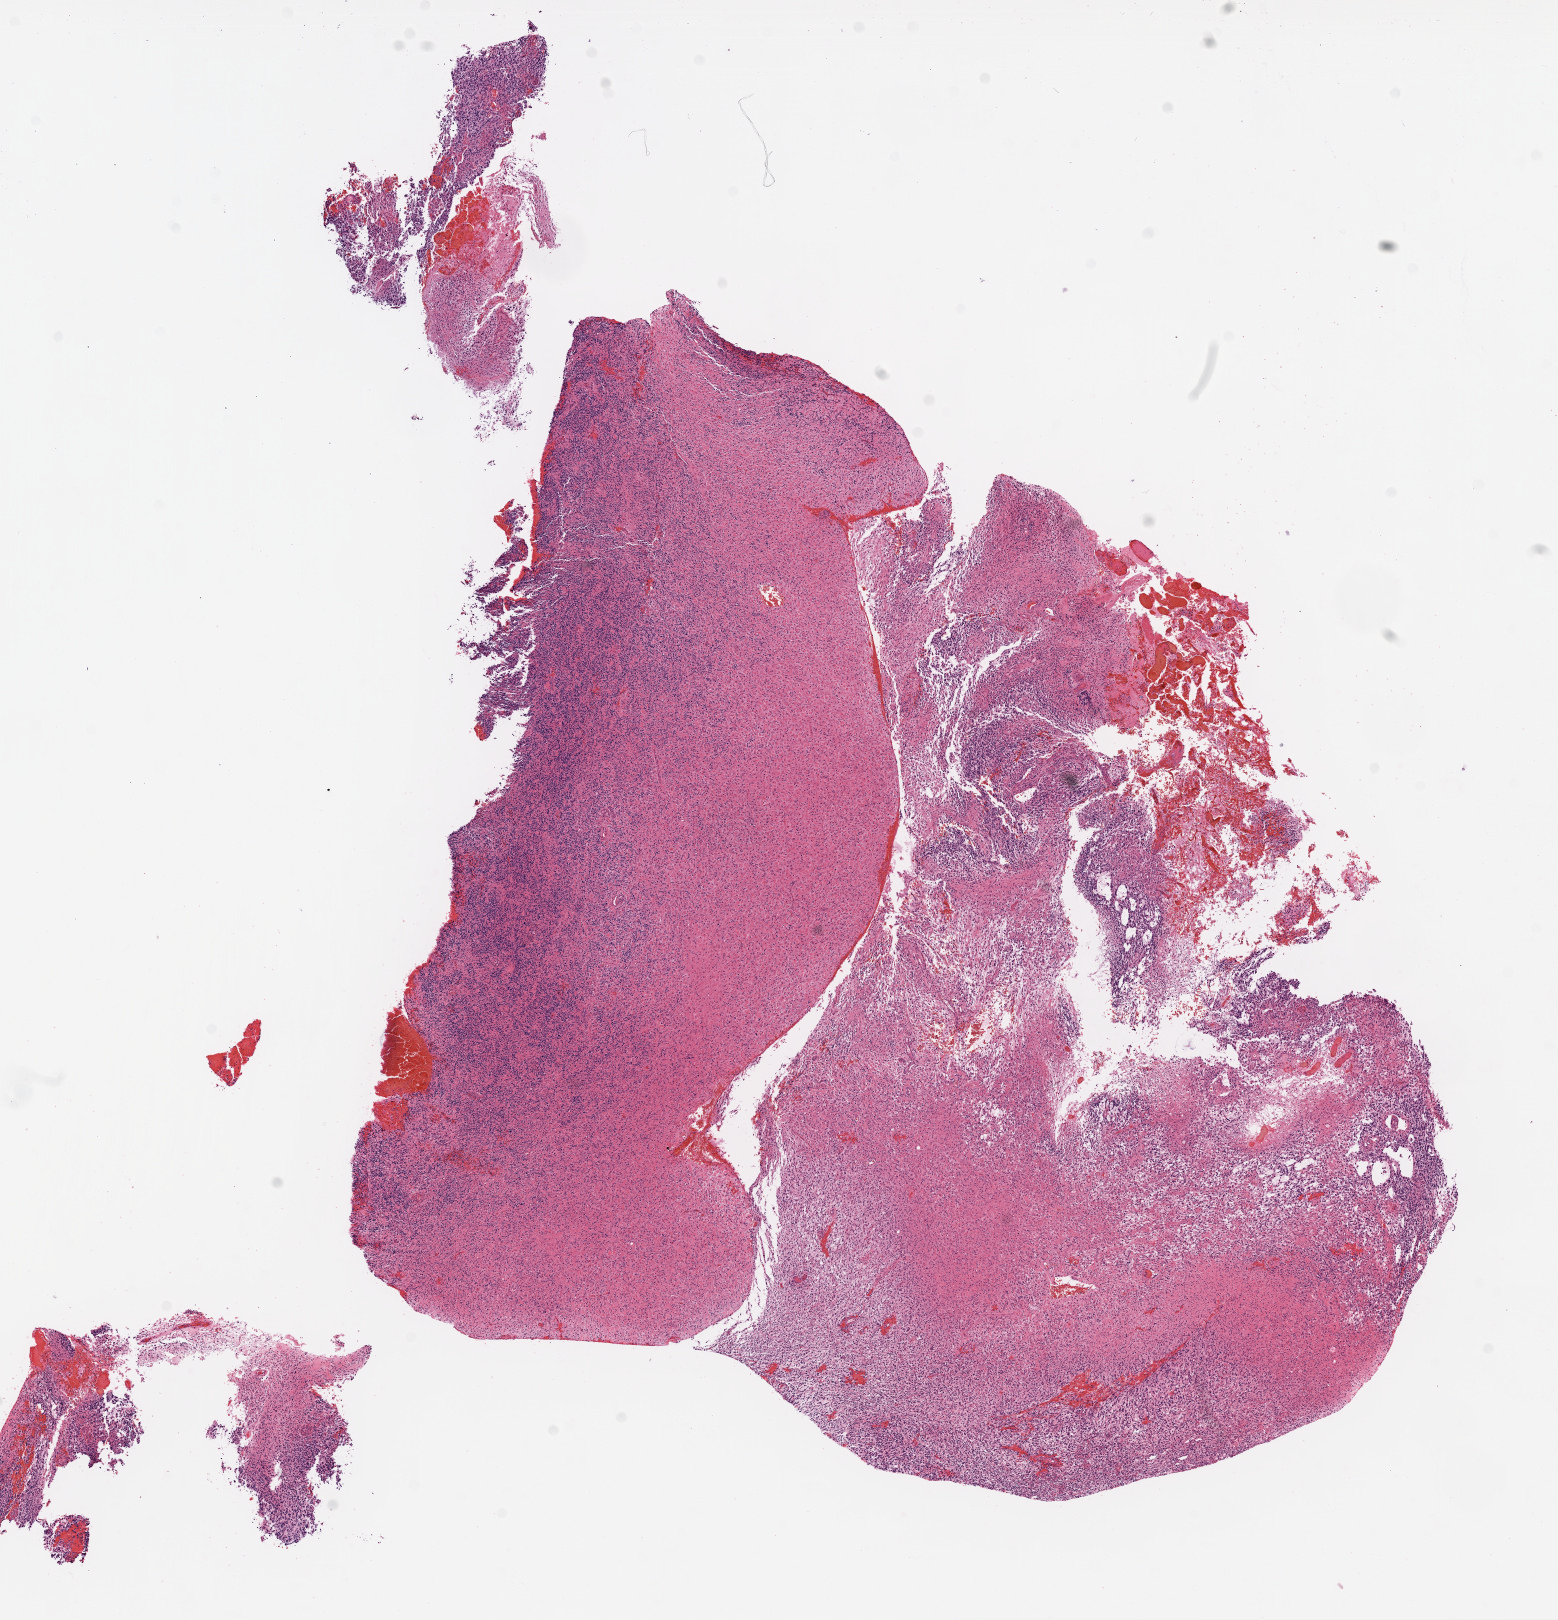
Whole-slide histology image, Hematoxylin and eosin (H&E) stained, low-resolution overview of the scanned area, about 12.6 x 13.1 mm; FFPE section; primary tumour sample from the brain. Male, age 31 years at initial diagnosis.
* pathologic diagnosis: Glioblastoma